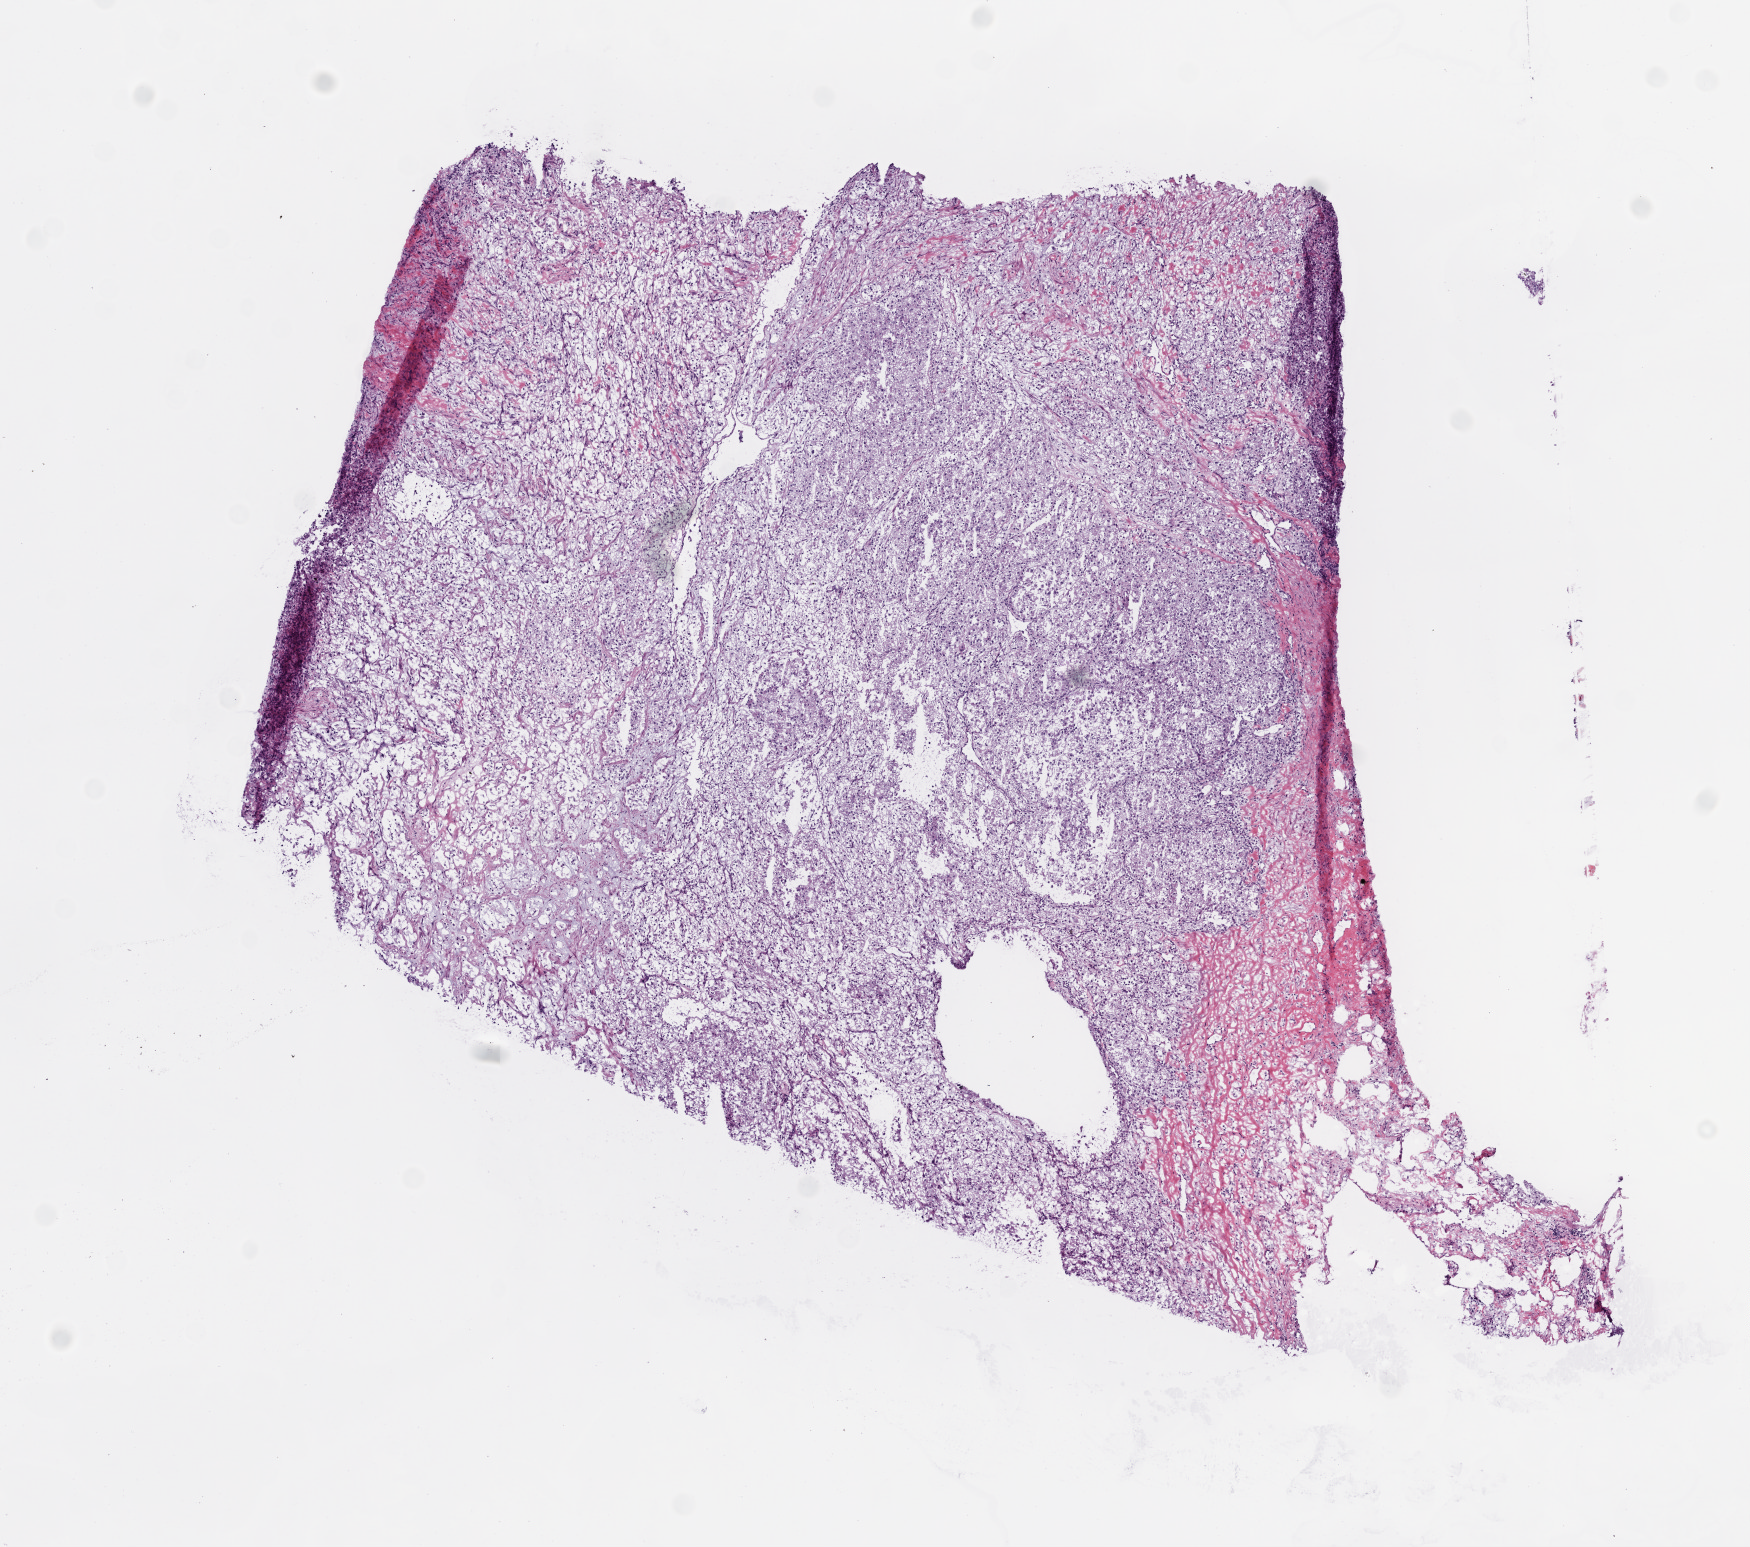
Whole-slide histology image, H&E-stained — shown as a low-resolution overview of the whole scanned area (about 7.0 x 6.2 mm, acquisition: 20x scan); frozen section from the top of the tissue portion; primary tumour sample from the kidney. Male patient; age at initial diagnosis 71 years.
Histologic diagnosis: Clear cell adenocarcinoma, NOS.